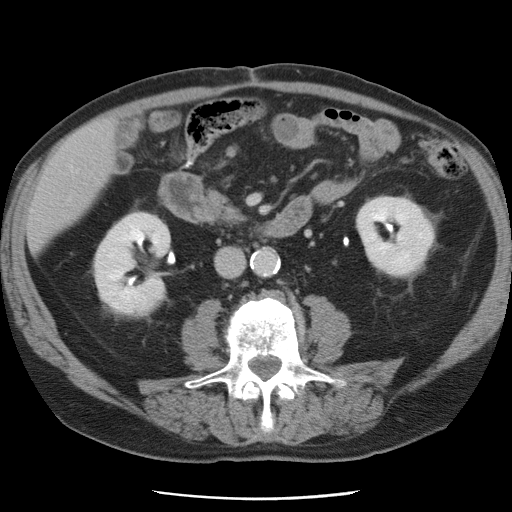
Contrast-enhanced abdominal CT, one axial slice; position 19 of 78 along the scan axis; intravenous contrast given; soft-tissue window (W 400 / L 40 HU); 512 × 512 image matrix, field of view 337 × 337 mm. Male patient, age 75 years. From the clinical record (not read from this slice): diagnosis: colorectal cancer liver metastases, imaged before liver resection; multiple liver metastases: yes; largest metastasis: 2.4 cm; disease in both lobes: yes.
Outlined on this slice (manually delineated by an expert):
- liver: bounding box <30,120,114,249> (left, top, right, bottom; pixels)
- planned liver remnant (the part of the liver to remain after resection): <29,121,114,249>